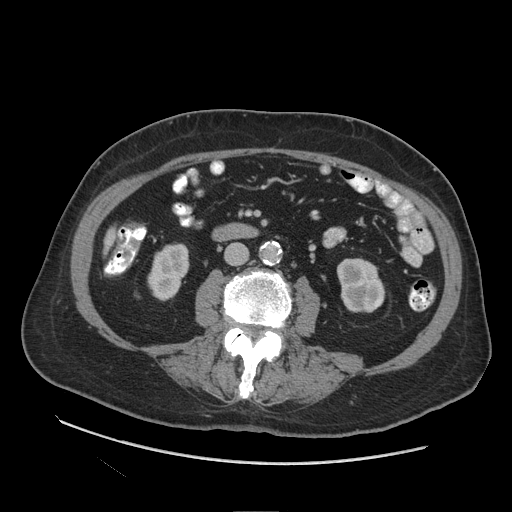
Contrast-enhanced abdominal CT (liver protocol), one axial slice. Reconstruction kernel STANDARD. 140 kVp. Soft-tissue window (W 400 / L 40 HU). 2.5 mm slice thickness. 512 × 512 image matrix, field of view 420 × 420 mm. Case-level facts recorded for this patient, not image findings: diagnosis: hepatocellular carcinoma (patient treated with transarterial chemoembolisation; whether this scan precedes or follows treatment is not stated here); TNM stage (as recorded): Stage-I; Child-Pugh class: A.
Structures marked on this image (semi-automatic segmentation, software-assisted and operator-edited):
- liver parenchyma outside the tumour (the mass and vessels are separate outlines, so this box may not span the whole liver): box from (x=104, y=228) to (x=114, y=253) px